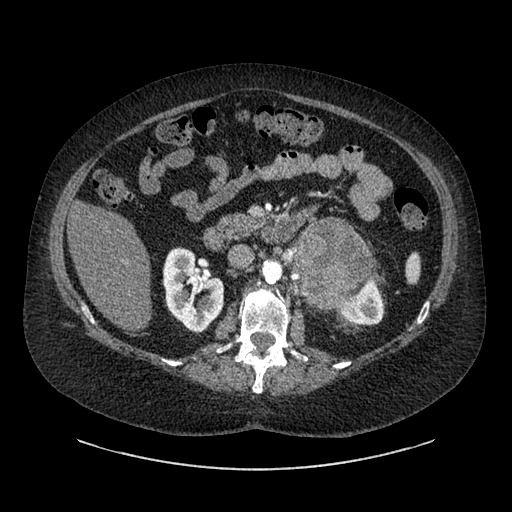
Contrast-enhanced abdominal CT, one axial slice. Position 521 of 769 along the scan axis. Reconstruction kernel SOFT. Intravenous contrast given. Soft-tissue window (W 400 / L 40 HU). 0.62 mm slice thickness. 512 × 512 image matrix, field of view 460 × 460 mm. Patient: female, 61 years. Case-level facts recorded for this patient, not image findings: diagnosis: adrenocortical carcinoma; tumour side: left adrenal; tumour size at pathology: 13 cm; Ki-67 index: 79 %; stage (as recorded): 2.
Structures marked on this image (semi-automatic segmentation, software-assisted and operator-edited):
- mass: bounding box [x1, y1, x2, y2] px = [292, 219, 372, 305]